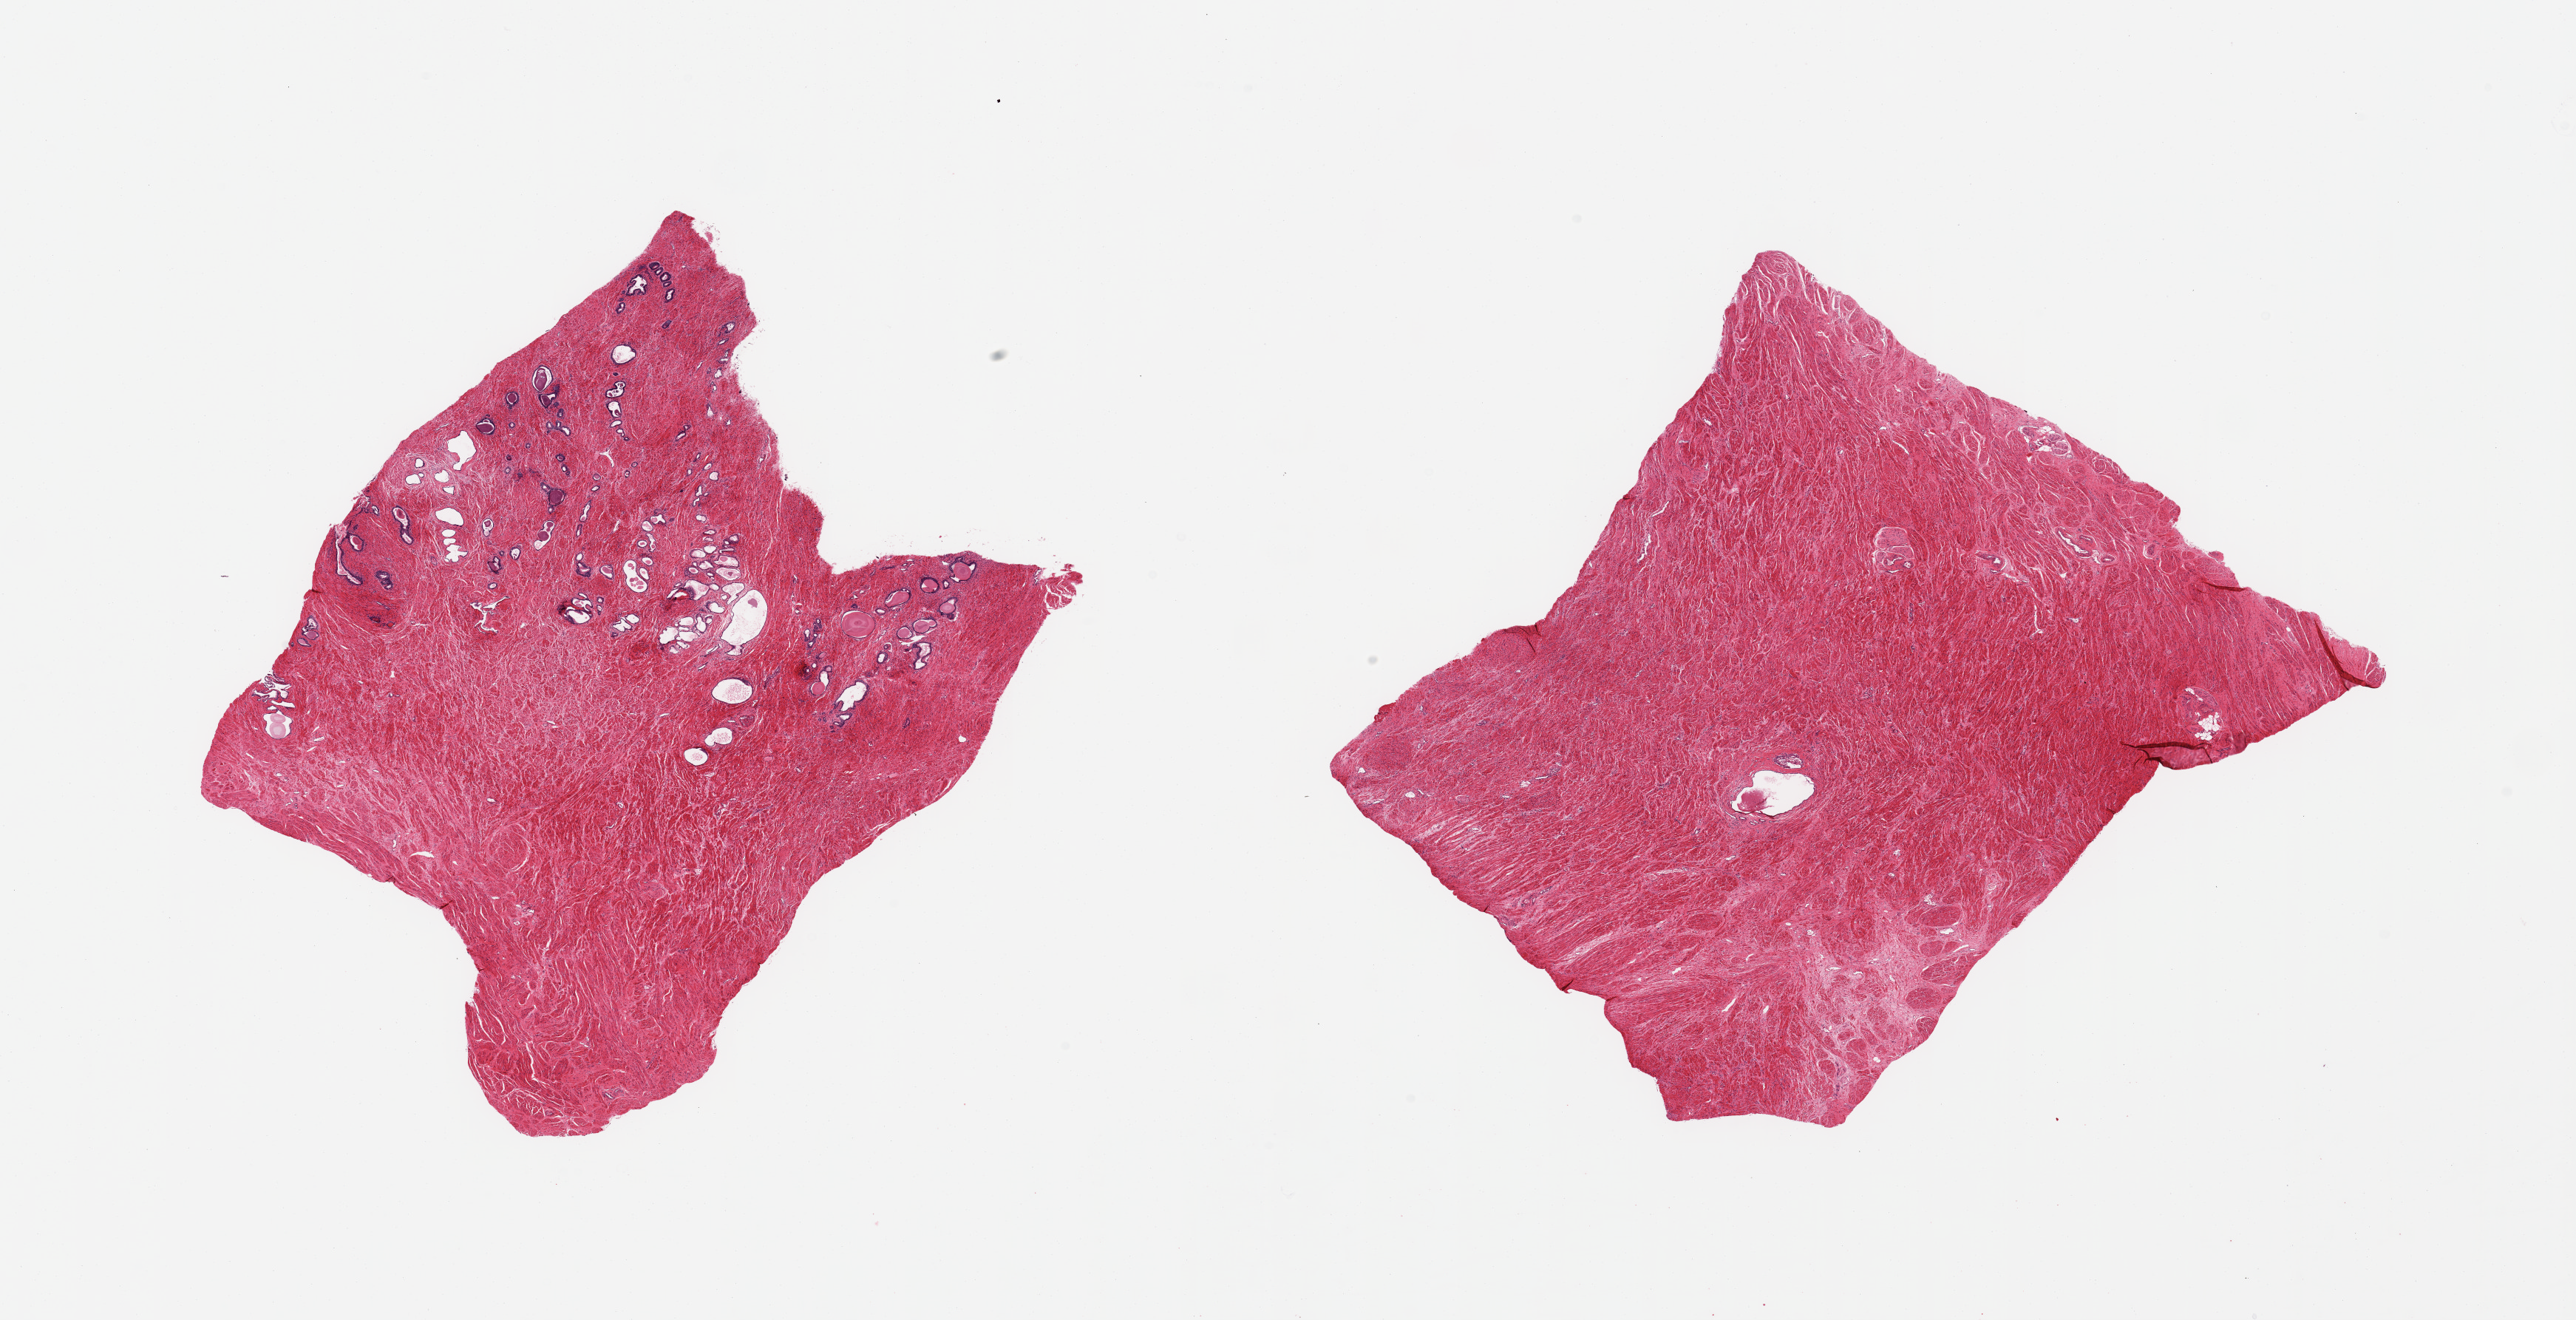
Haematoxylin and eosin whole-slide image, brightfield, shown as a low-resolution overview of the whole scanned area (about 27.6 x 14.1 mm); PAXgene-fixed paraffin-embedded (PFPE) section; target tissue: prostate; donor tissue sample. Donor: male.
- review note (as recorded): 2 pieces, ~80% prostatic stroma